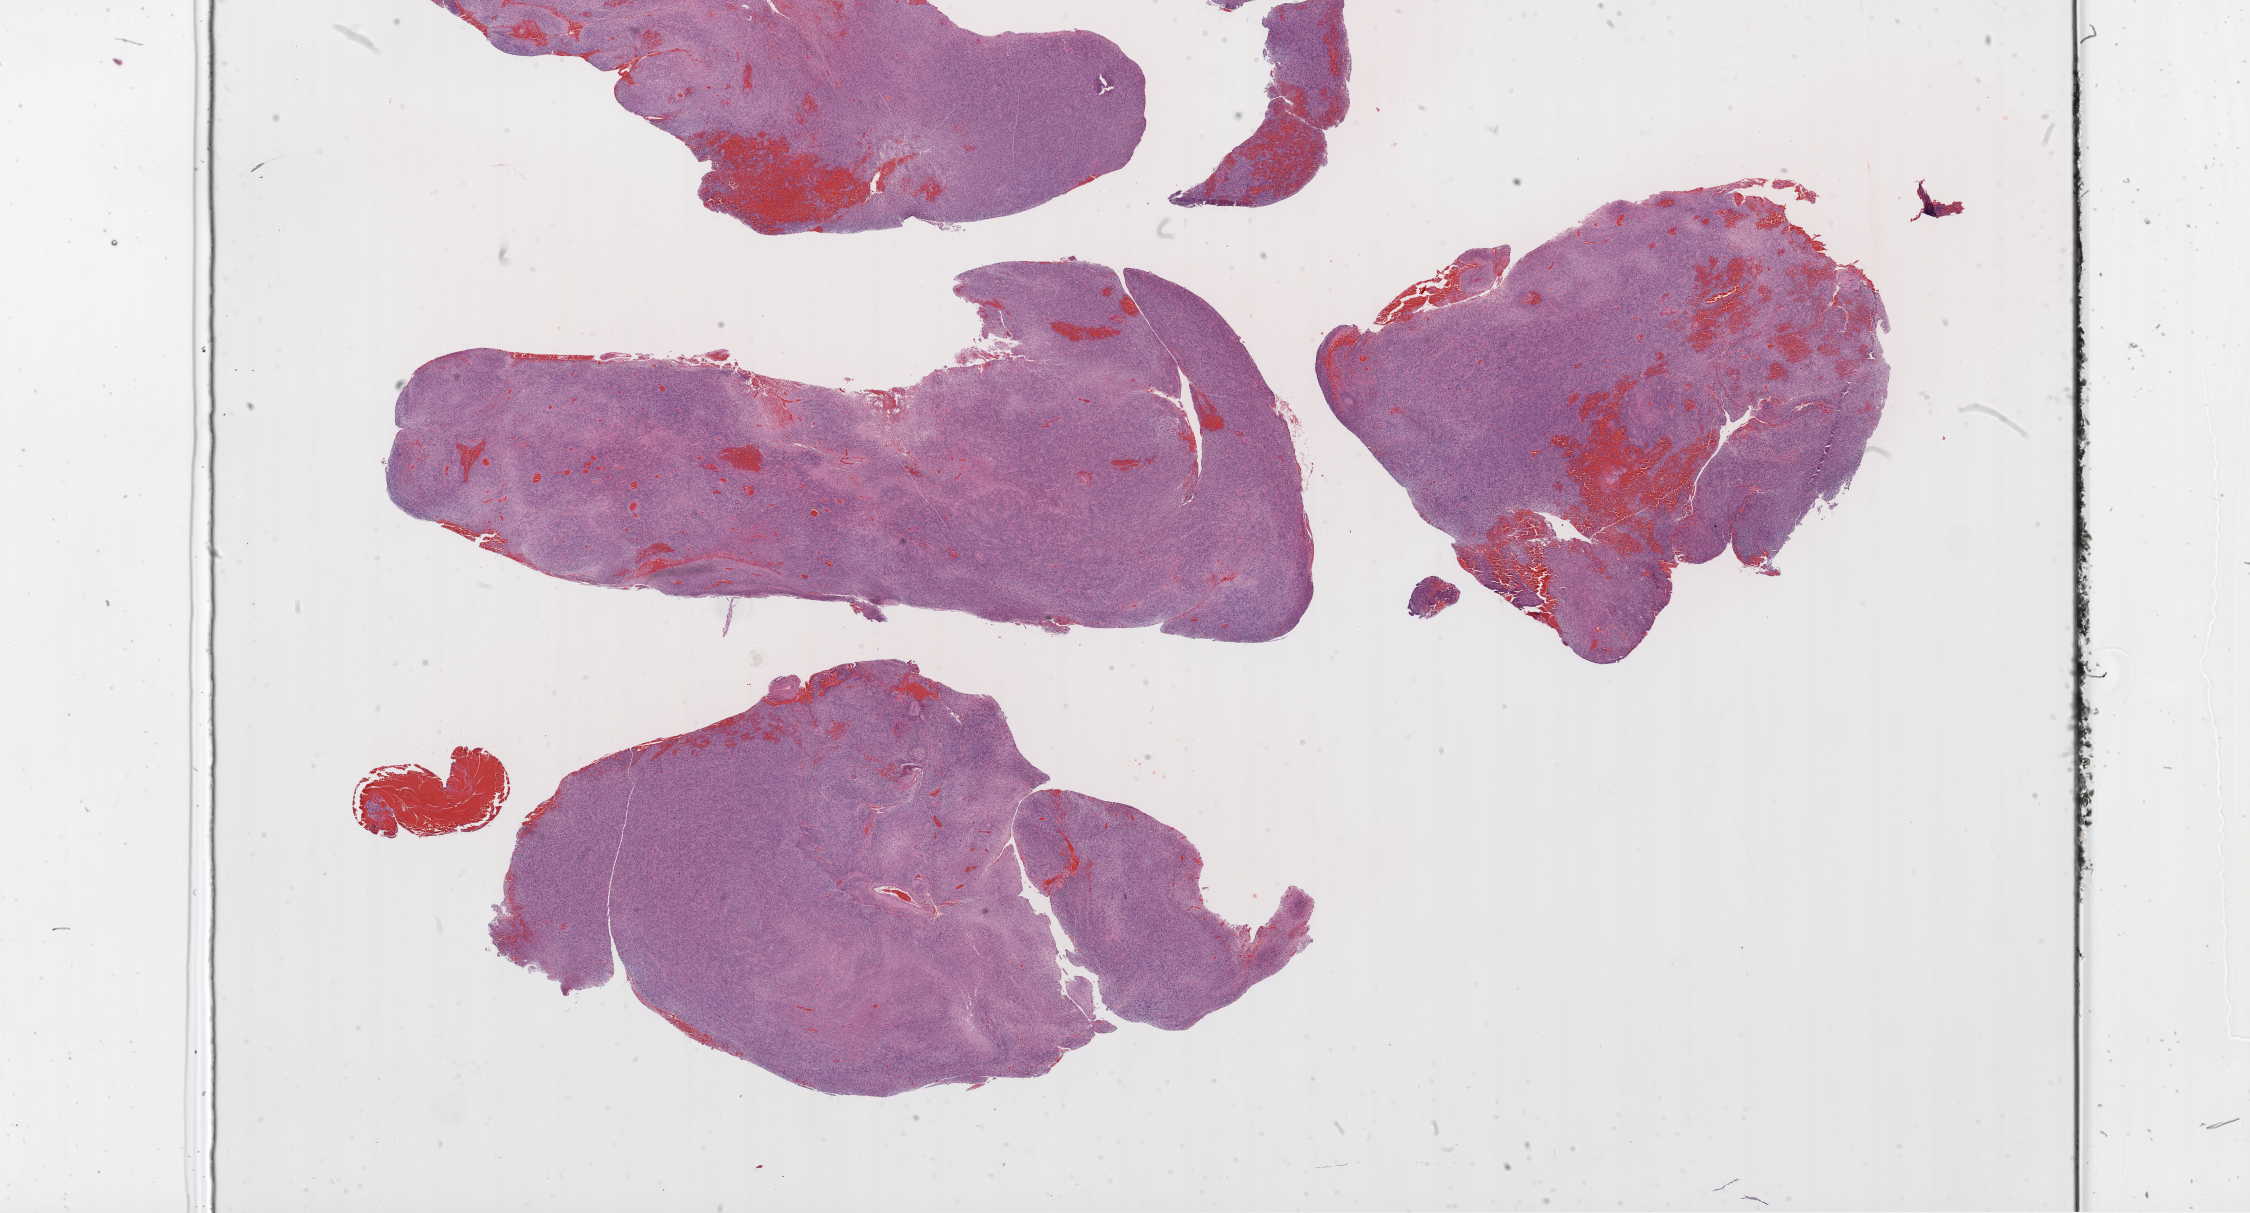
Hematoxylin and eosin (H&E) stained whole-slide image — whole scanned area (about 36.1 x 19.5 mm, from a 20x scan) shown as a low-resolution overview; formalin-fixed paraffin-embedded (FFPE) diagnostic section; primary tumour sample from the brain. Male, age 53 years at initial diagnosis.
Histologic diagnosis: Glioblastoma.